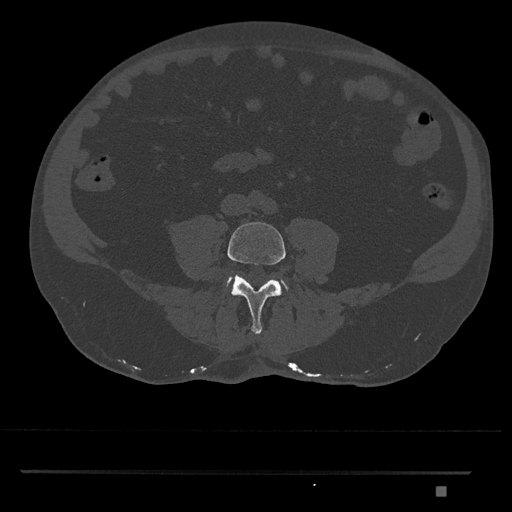
CT including the spine, one axial slice. Slice 606 of 1134 in the series (ordered by position). Reconstruction kernel Br40s/3. 120 kVp. Bone window (W 1800 / L 400 HU). 0.5 mm slice thickness. 512 × 512 image matrix, field of view 429 × 429 mm. Male patient, age 65 years. Case-level facts recorded for this patient, not image findings: primary cancer: prostate.
Structures marked on this image (semi-automatically segmented with operator editing):
- L4 vertebra: bounding box [x1, y1, x2, y2] px = [227, 222, 286, 335]
- L5 vertebra: [227, 278, 288, 290]